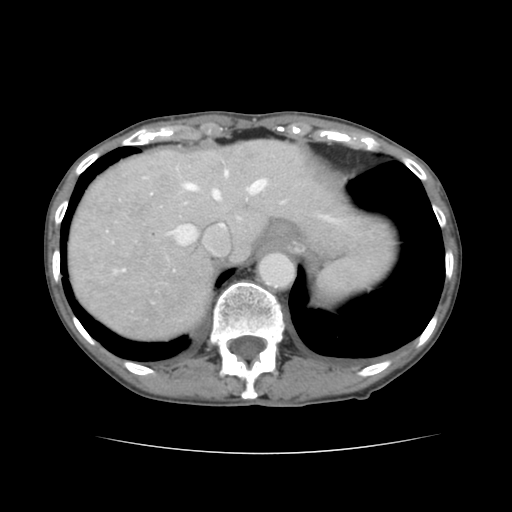
Contrast-enhanced abdominal CT, one axial slice. Slice 116 of 136 in the series (ordered by position). Intravenous contrast given. Soft-tissue window (W 400 / L 40 HU). 512 × 512 image matrix, field of view 319 × 319 mm. Female patient, age 77 years. From the clinical record (not read from this slice): diagnosis: colorectal cancer liver metastases, imaged before liver resection; multiple liver metastases: yes; largest metastasis: 3 cm; disease in both lobes: no.
Annotated regions visible in this slice (manually delineated by an expert):
- hepatic veins: bounding box (x1, y1, x2, y2) in pixels: (142, 171, 266, 255)
- liver: (69, 140, 391, 339)
- planned liver remnant (the part of the liver to remain after resection): (172, 140, 392, 257)